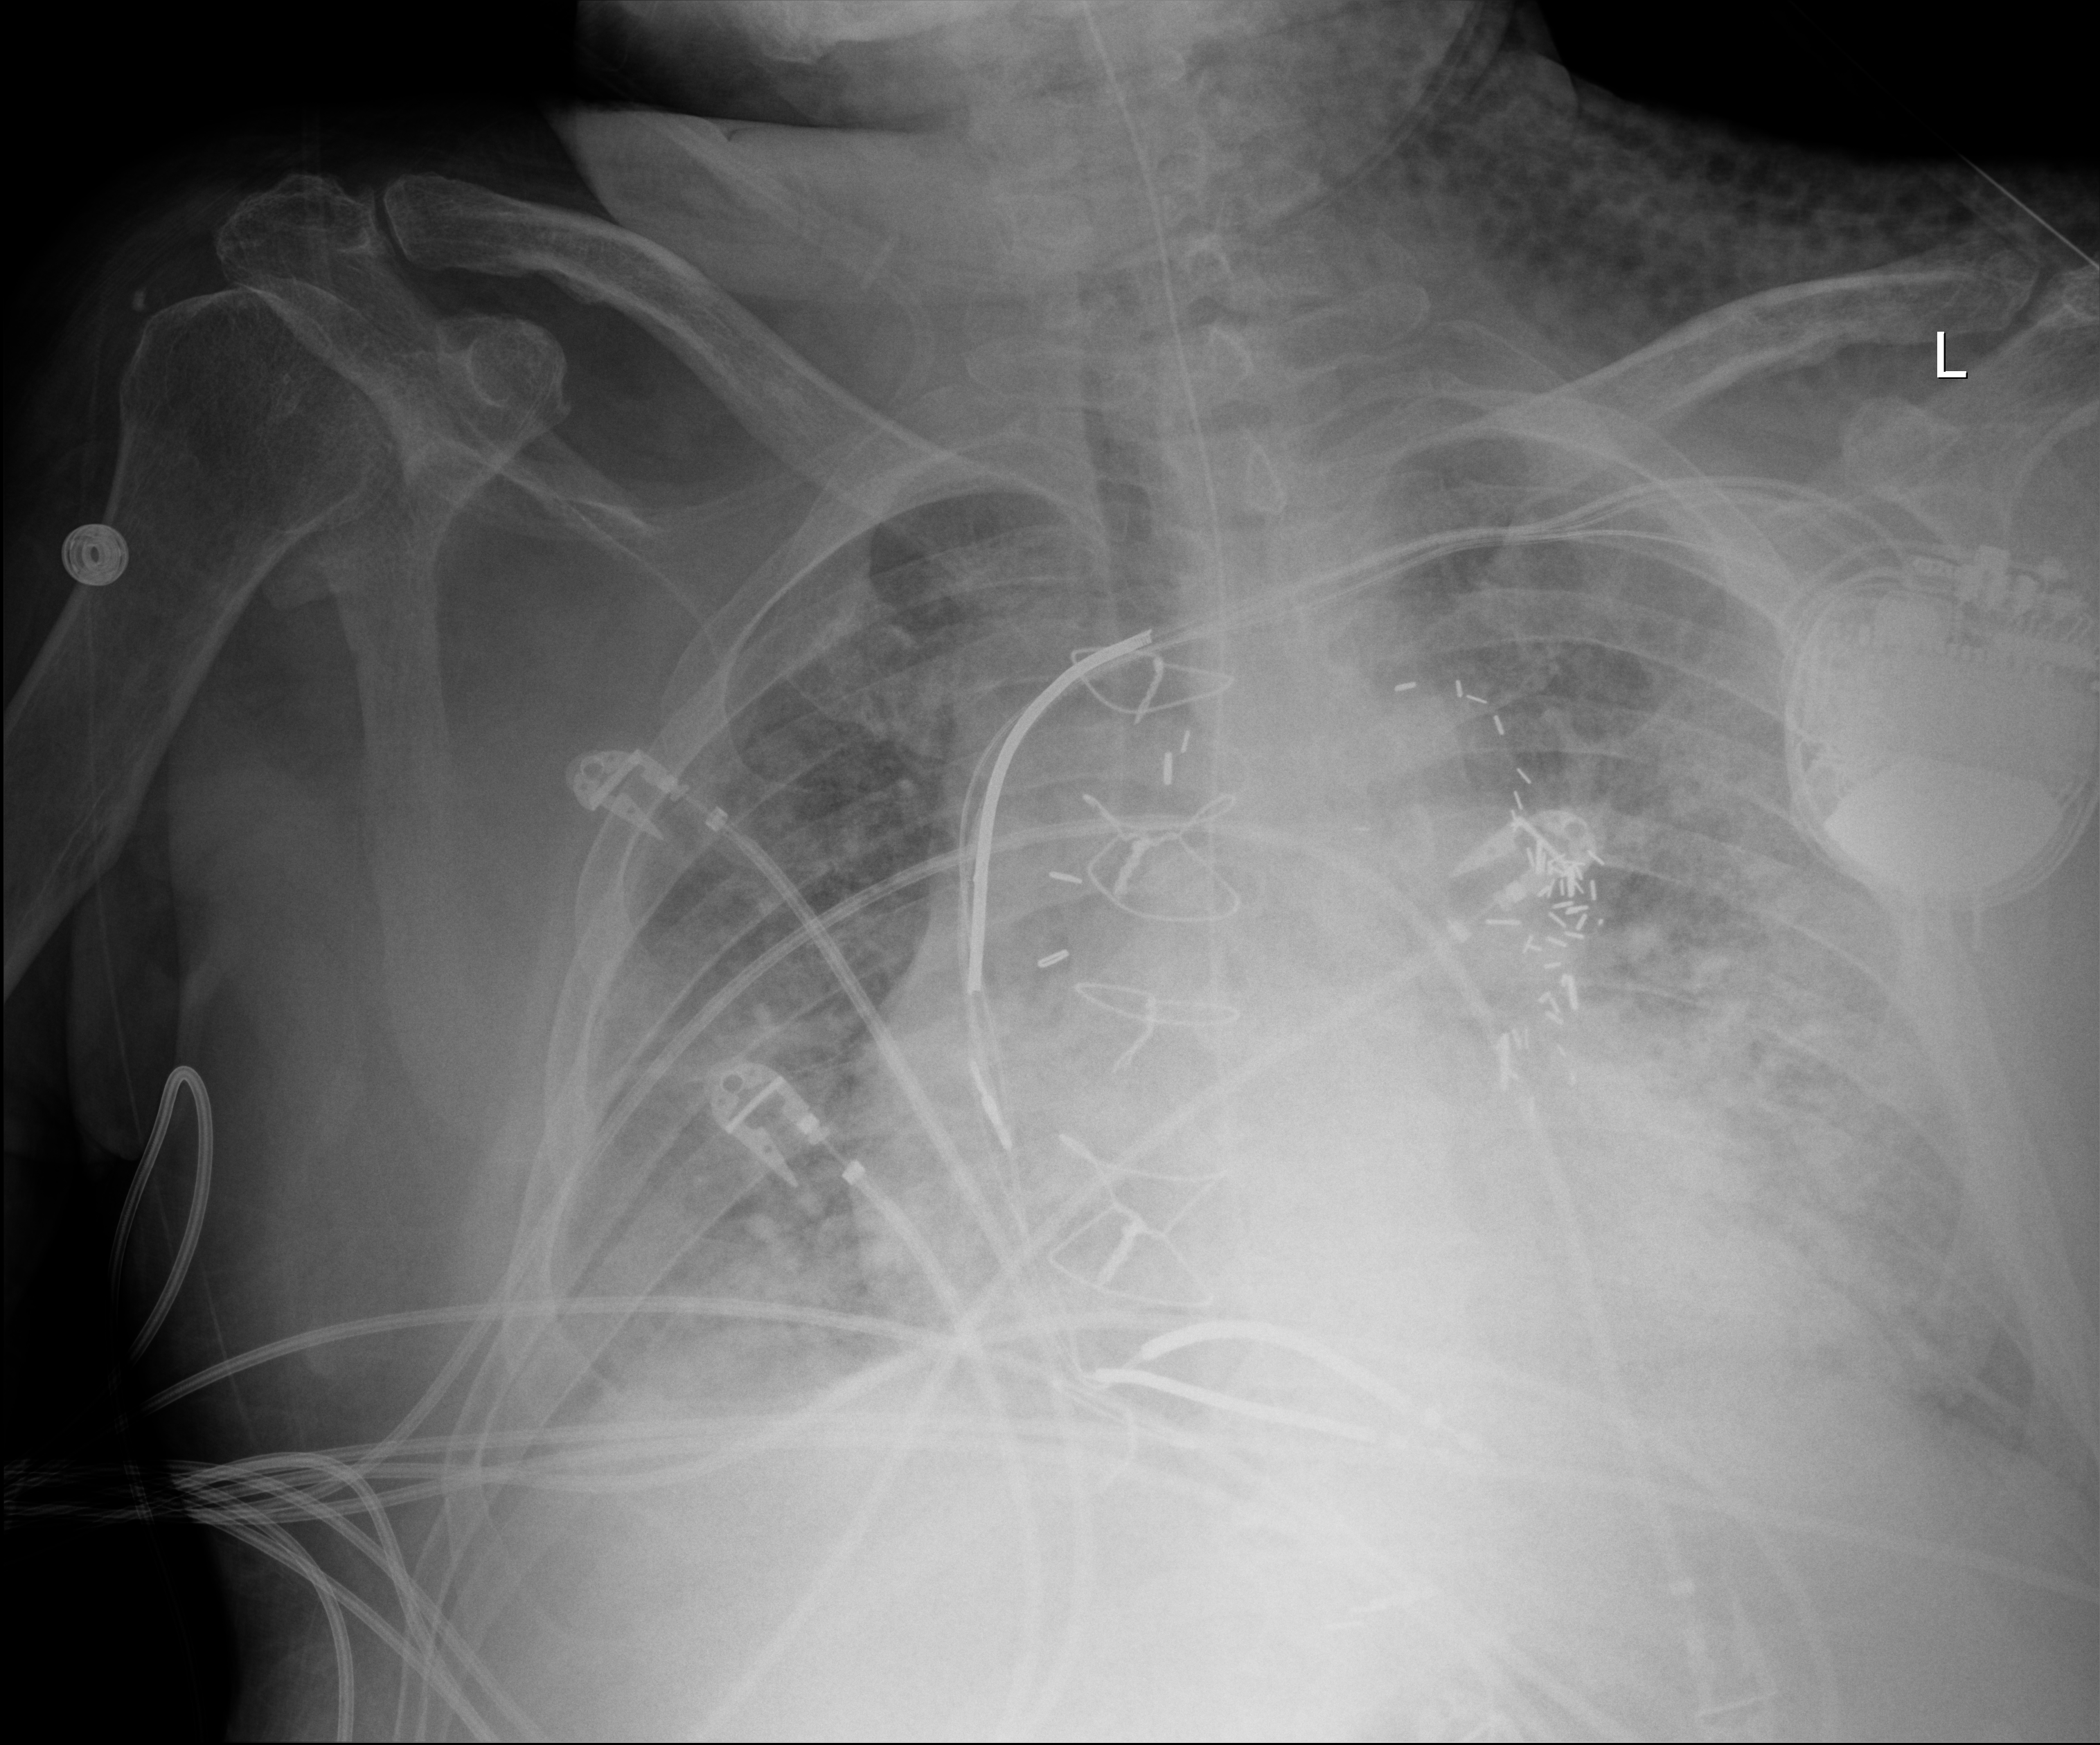
Bedside chest radiograph (digital radiography); anteroposterior (AP) projection. Male patient hospitalised with COVID-19, age 60–74 years.
From the hospital-stay record, not from the radiograph (when in the stay this image was taken is not recorded):
- mechanically ventilated during this hospital stay: yes
- admitted to intensive care during this hospital stay: yes